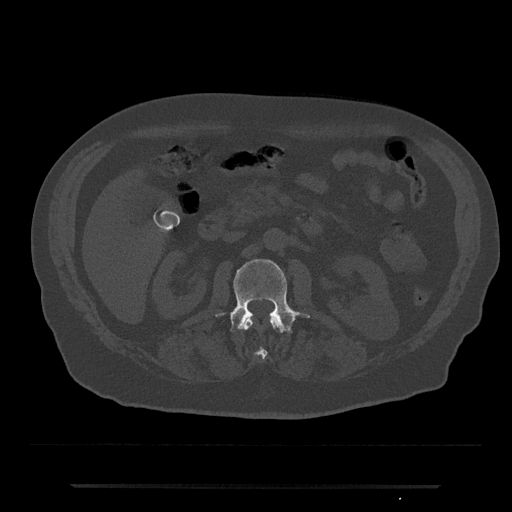
CT including the spine, one axial slice. Slice 488 of 797 in the series (ordered by position). Reconstruction kernel Br40s/3. 120 kVp. Bone window (W 1800 / L 400 HU). 0.5 mm slice thickness. 512 × 512 image matrix, field of view 434 × 434 mm. Patient: male, 80 years. From the clinical record (not read from this slice): primary cancer: prostate.
Outlined on this slice (semi-automatically segmented with operator editing):
- L1 vertebra: bounding box <242,317,282,358> (left, top, right, bottom; pixels)
- L2 vertebra: <215,259,310,333>